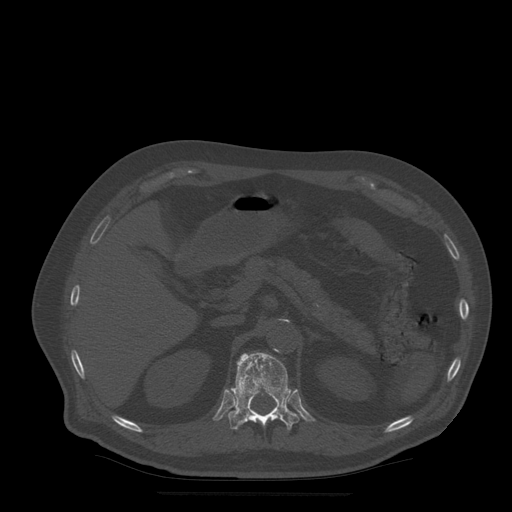
CT including the spine, one axial slice. Bone window (W 1800 / L 400 HU). 1.25 mm slice thickness. 512 × 512 image matrix. Patient age 72 years. Case-level facts recorded for this patient, not image findings: primary cancer: prostate.
Annotated regions visible in this slice (semi-automatically segmented with operator editing):
- T12 vertebra: bounding box (x1, y1, x2, y2) in pixels: (228, 353, 300, 430)